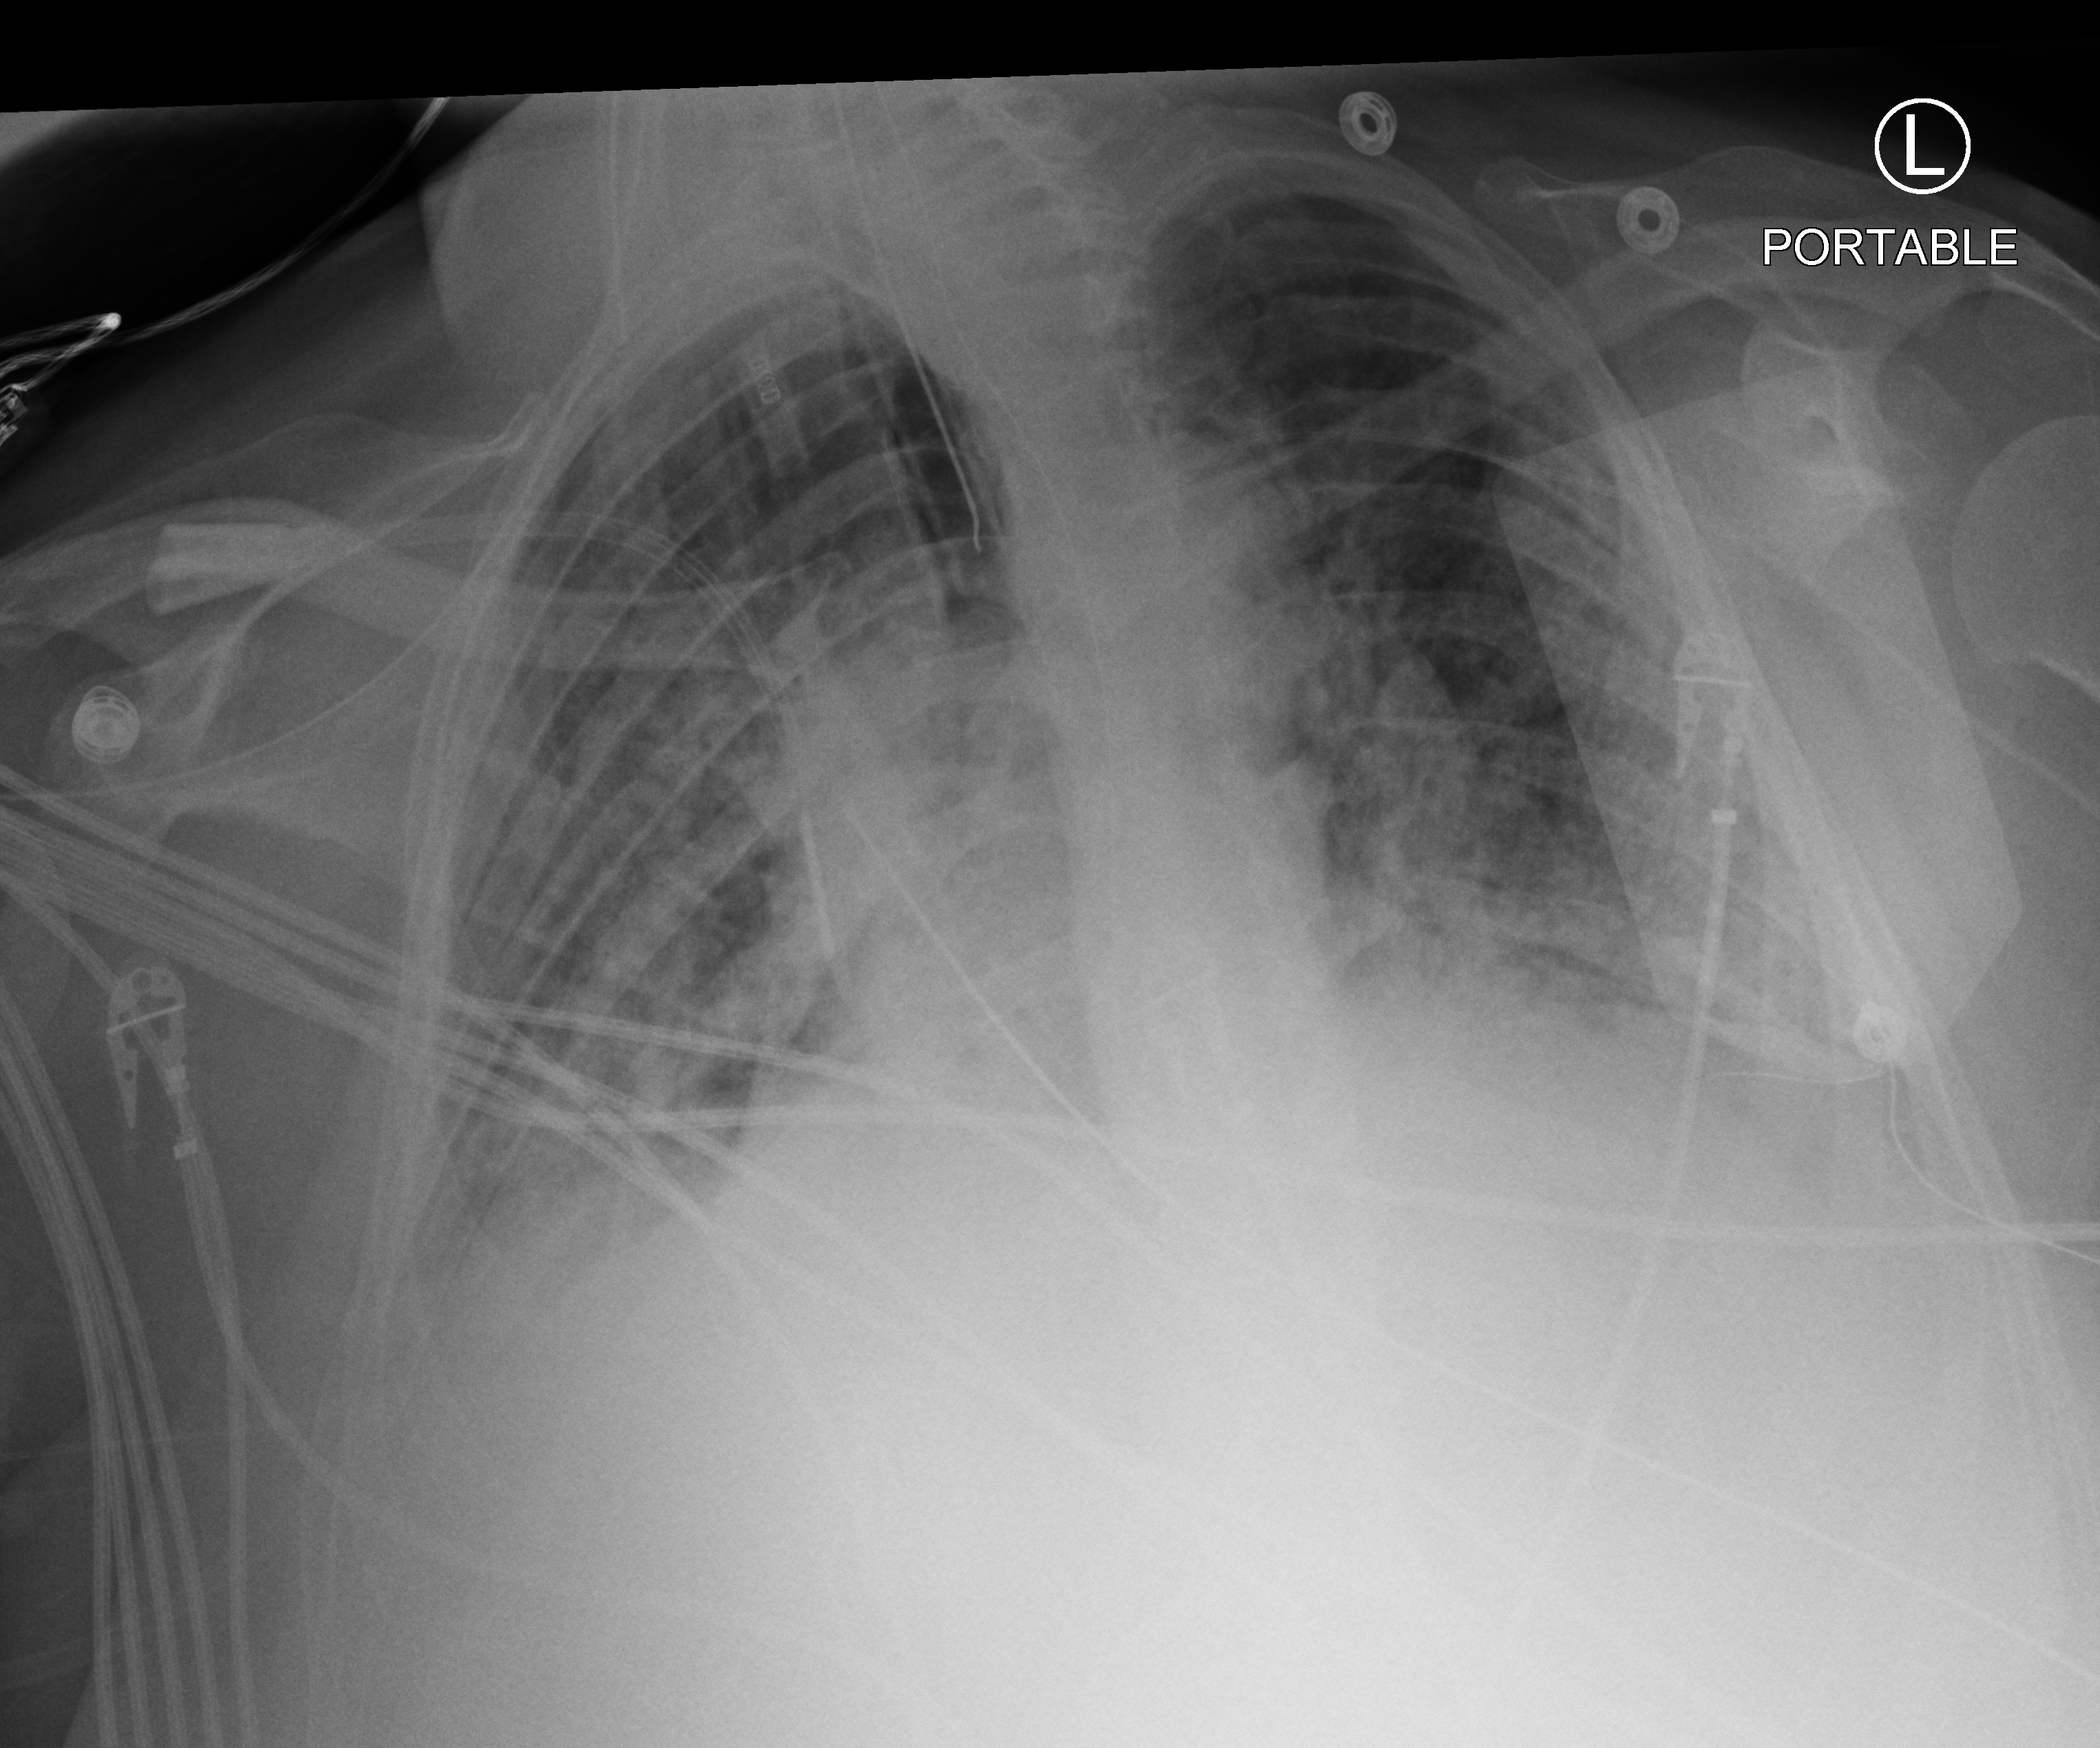
Portable chest radiograph, anteroposterior (AP) projection. Male patient hospitalised with COVID-19, age 18–59 years.
Hospital-stay facts (about this admission, not read from this image; timing relative to this image not recorded): admitted to intensive care during this hospital stay: yes; length of hospital stay: 39 days; mechanically ventilated during this hospital stay: yes.